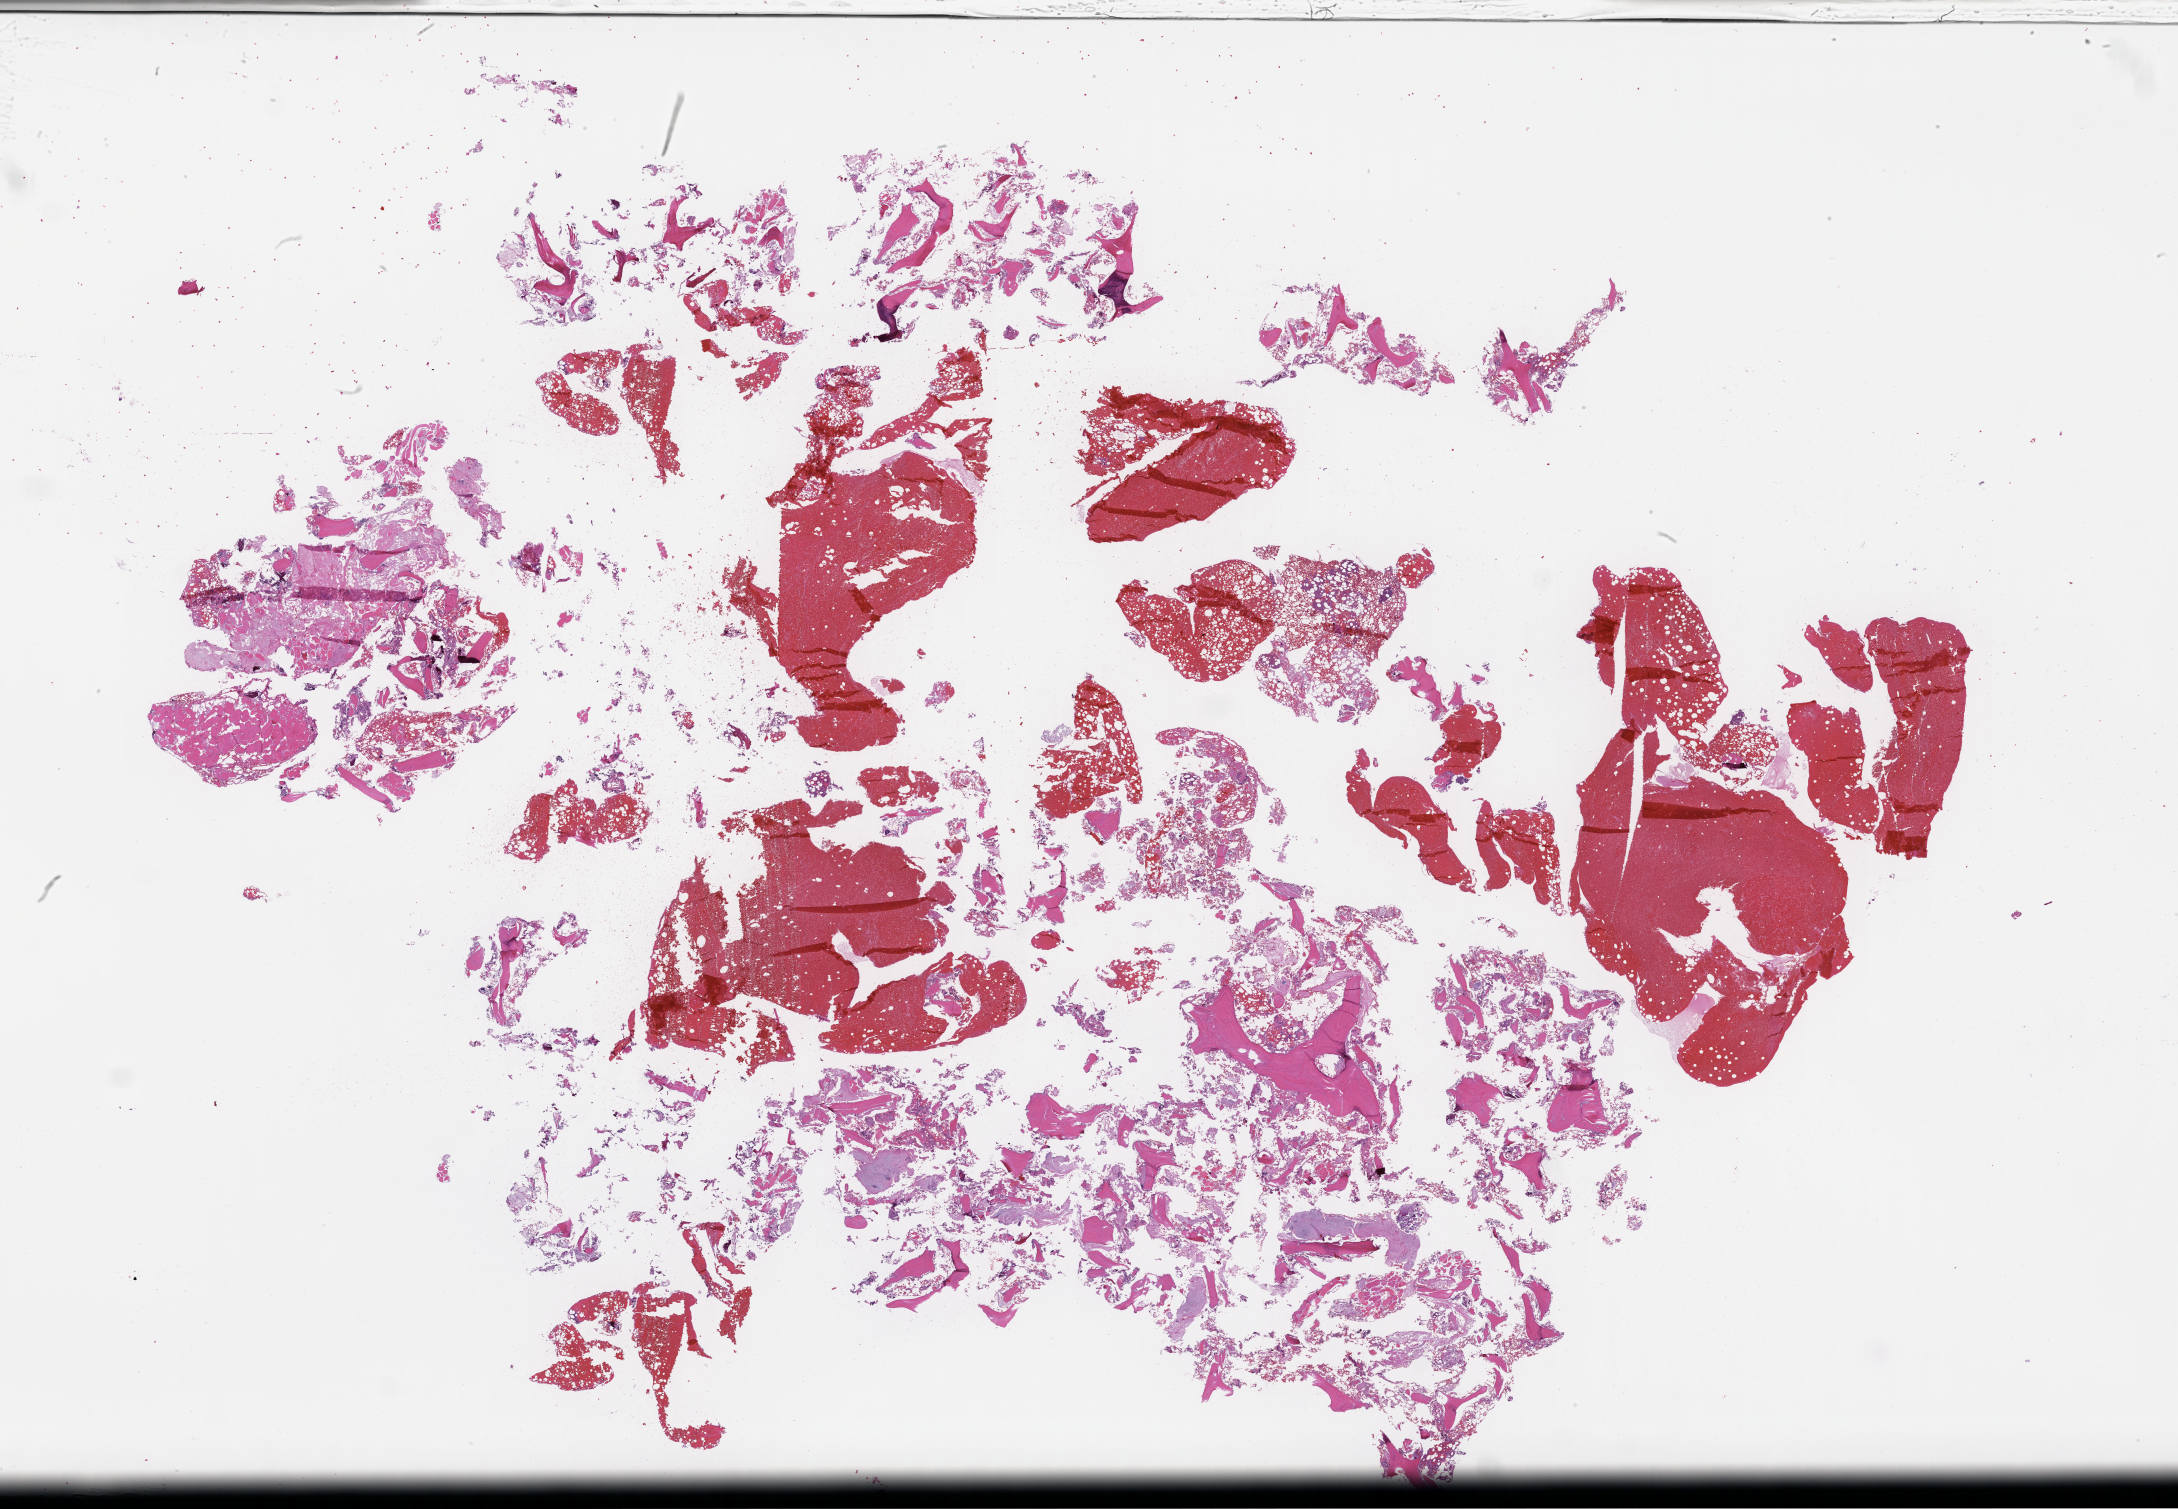
Digitized hematoxylin and eosin (H&E)-stained section — whole scanned area (about 35.2 x 24.4 mm) shown as a low-resolution overview. Formalin-fixed, paraffin-embedded (FFPE) tissue. Site: bone. Specimen time point: archival tissue. Patient sex: female.
This section: primary tumor. Diagnosis: Plasma Cell Myeloma.